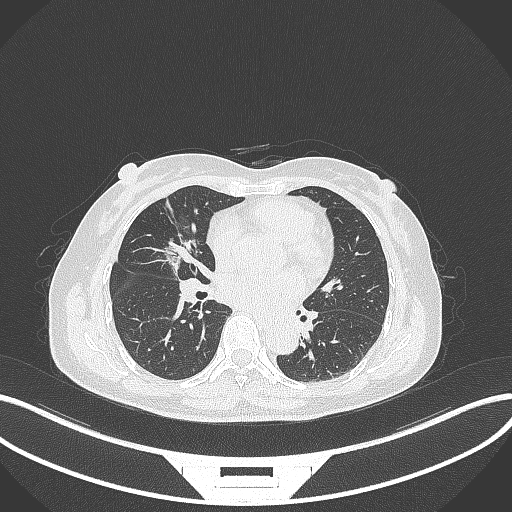
Chest CT, one axial slice; position 142 of 284 along the scan axis; reconstruction kernel B70f; lung window (W 1500 / L -600 HU); 1 mm slice thickness; 512 × 512 image matrix, field of view 400 × 400 mm. Female patient, age 51 years. From the clinical record (not read from this slice): clinical TNM (as recorded): T1c N0 M0; histopathological grade: G2.
Structures marked on this image (bounding box drawn by a radiologist):
- lung tumour (recorded histology: adenocarcinoma): bounding box [x1, y1, x2, y2] px = [159, 233, 193, 276]